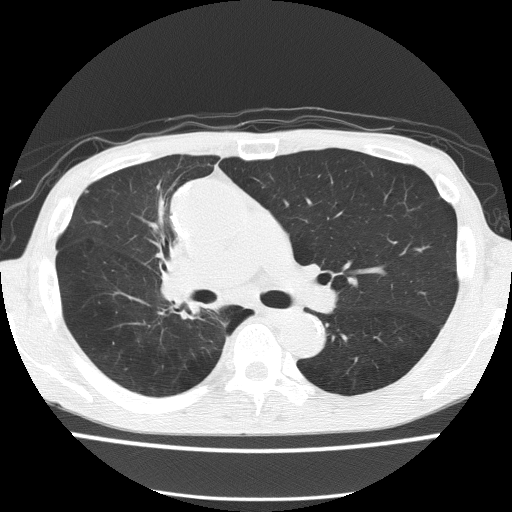
Low-dose screening chest CT, one axial slice. Slice 91 of 150 in the series (ordered by position). Reconstruction kernel FC51. 120 kVp. Lung window (W 1500 / L -600 HU). 2 mm slice thickness. 512 × 512 image matrix, field of view 336 × 336 mm.
Annotated regions visible in this slice (manually delineated by an expert):
- lesion 1 (tumor, hilum of right lung): bounding box <162,243,197,301> (left, top, right, bottom; pixels)